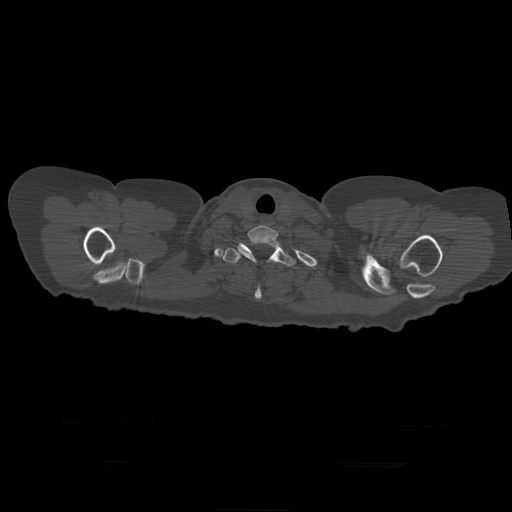
CT including the spine, one axial slice; position 381 of 399 along the scan axis; reconstruction kernel STANDARD; 120 kVp; bone window (W 1800 / L 400 HU); 512 × 512 image matrix. Patient age 41 years. From the clinical record (not read from this slice): primary cancer: breast.
Annotated regions visible in this slice (semi-automatically segmented with operator editing):
- T1 vertebra: bounding box (x1, y1, x2, y2) in pixels: (237, 225, 279, 268)
- T2 vertebra: (223, 239, 296, 299)